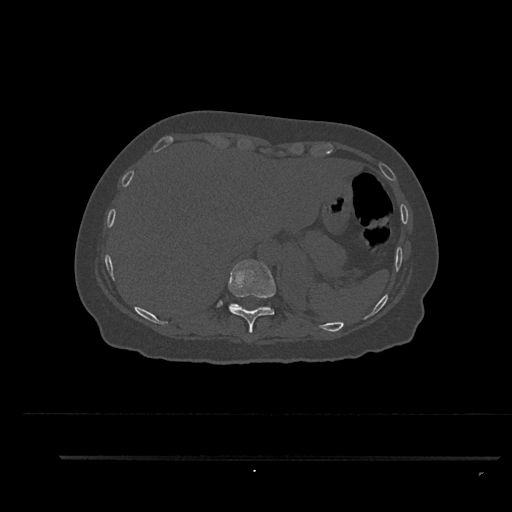
CT including the spine, one axial slice. Slice 355 of 797 in the series (ordered by position). Reconstruction kernel Br40s/3. 120 kVp. Bone window (W 1800 / L 400 HU). 0.5 mm slice thickness. 512 × 512 image matrix, field of view 408 × 408 mm. Patient: female, 44 years. Case-level facts recorded for this patient, not image findings: primary cancer: renal.
Annotated regions visible in this slice (semi-automatic segmentation, software-assisted and operator-edited):
- T10 vertebra: bounding box [x1, y1, x2, y2] px = [228, 259, 276, 333]
- T11 vertebra: [231, 304, 238, 305]